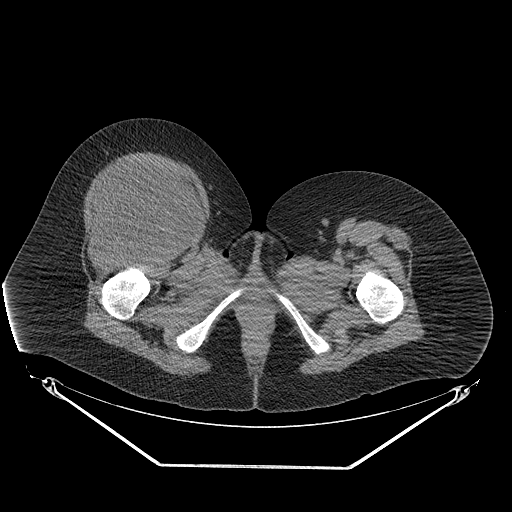
CT of an extremity soft-tissue mass (from a PET/CT study), one axial slice; slice 54 of 267 in the series (ordered by position); reconstruction kernel STANDARD; soft-tissue window (W 400 / L 40 HU); 3.75 mm slice thickness; 512 × 512 image matrix, field of view 500 × 500 mm. Female patient. Case-level facts recorded for this patient, not image findings: histological type: malignant solitary fibrous tumor; grade: intermediate; site of the primary tumour: right thigh.
Annotated regions visible in this slice (expert contour drawn on MRI and transferred to this co-registered scan by the dataset authors):
- gross tumour volume including surrounding oedema: bounding box [x1, y1, x2, y2] px = [80, 160, 197, 243]
- gross tumour volume (mass): [80, 162, 193, 241]